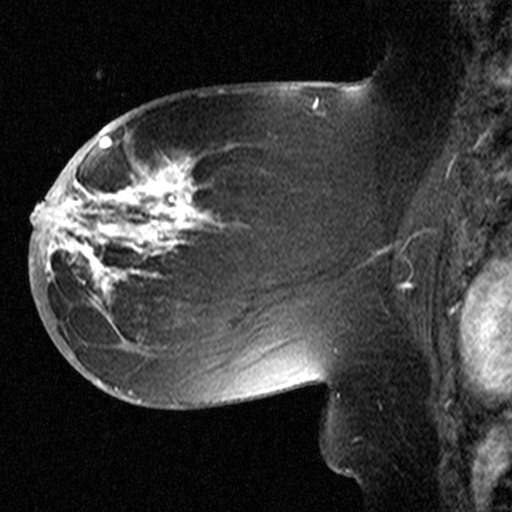
Breast MRI (dynamic contrast-enhanced), one sagittal slice. Slice 23 of 44 in the series (ordered by position). Dynamic contrast-enhanced study with each time point stored as its own series, time point 2 of 3 at this slice position (early post-contrast, ordered by acquisition time). 1.5 T. TE 4.5 ms, TR 11 ms. 512 × 512 image matrix. Patient: female, 53 years. From the clinical record (not read from this slice): setting: breast cancer imaged before/during neoadjuvant chemotherapy; receptor status: HR-positive, HER2-negative.
Annotated regions visible in this slice (semi-automatic segmentation, software-assisted and operator-edited):
- analysis volume of interest (the breast-tissue region the enhancement analysis was run in; not a lesion): bounding box <58,154,311,367> (left, top, right, bottom; pixels)
- tumour enhancement mask (voxels above the 90 % enhancement threshold inside the analysis volume of interest): <58,165,199,300>